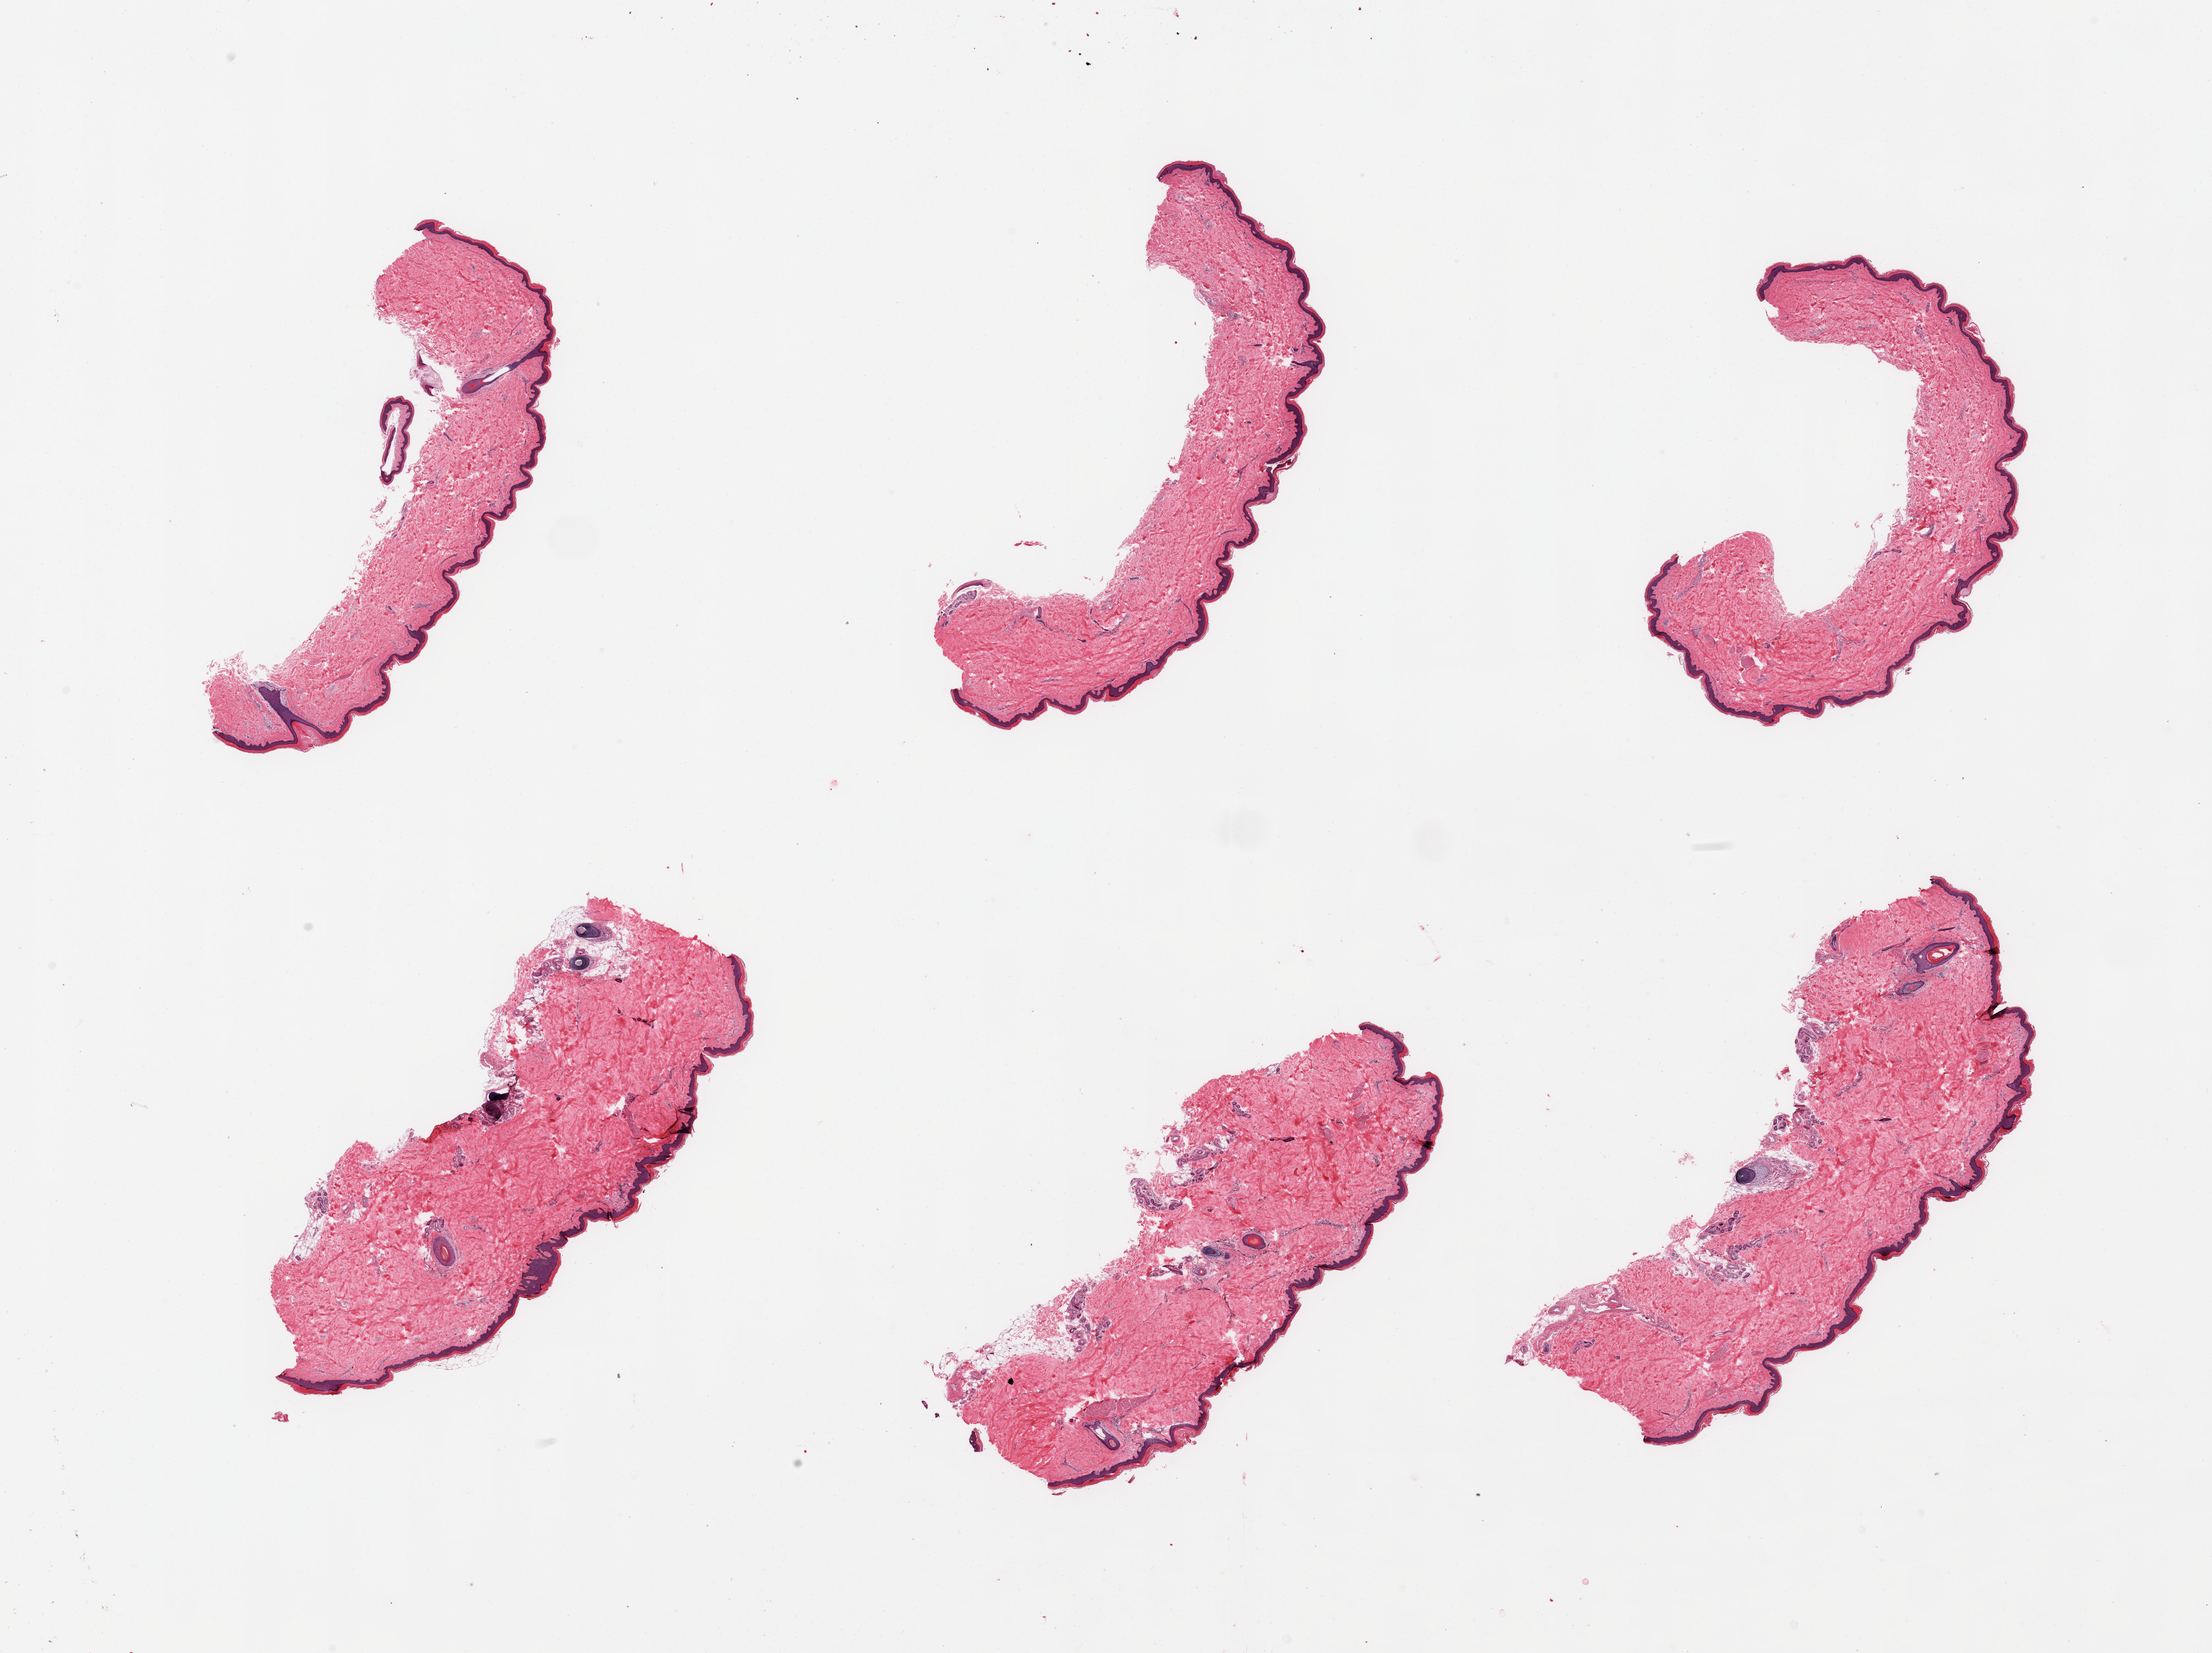
Digitized hematoxylin and eosin (H&E)-stained section — shown as a low-resolution overview of the whole scanned area (about 26.6 x 19.9 mm); PAXgene-fixed paraffin-embedded (PFPE) section; section of skin of lower leg (target tissue); tissue donor sample. Male donor.
Pathologist's review note for this sample: 6 pieces; well trimmed, epidermis measured 38 microns.